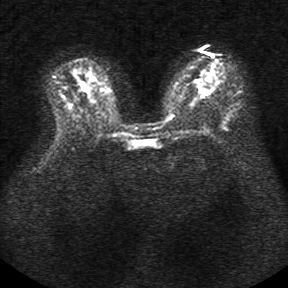
Breast MRI, one axial slice; slice 18 of 34 in the series (ordered by position); diffusion-weighted series; image 2 of 4 stored at this slice position (different b-values; order by instance number); 1.5 T; 288 × 288 image matrix, field of view 340 × 340 mm. Female patient.
Annotated regions visible in this slice (manually delineated by an expert):
- tumour on diffusion-weighted imaging: box from (x=204, y=92) to (x=210, y=95) px